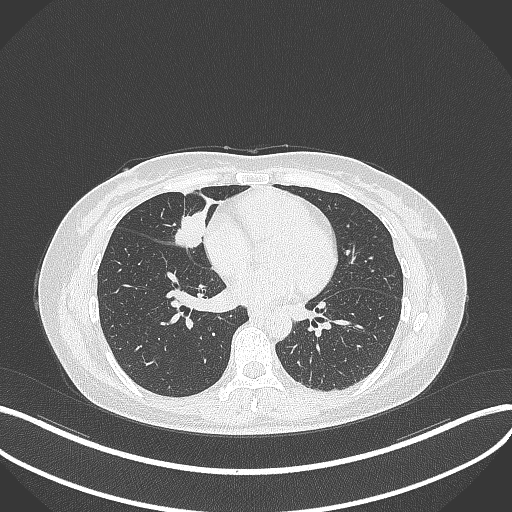
Chest CT, one axial slice. Position 121 of 284 along the scan axis. Reconstruction kernel B70f. 120 kVp. Lung window (W 1500 / L -600 HU). 1 mm slice thickness. 512 × 512 image matrix, field of view 400 × 400 mm. Female patient, age 43 years. Case-level facts recorded for this patient, not image findings: clinical TNM (as recorded): T1c N3 M1.
Structures marked on this image (rectangle marked by the reading radiologist):
- lung tumour (recorded histology: adenocarcinoma): bounding box <167,208,211,254> (left, top, right, bottom; pixels)